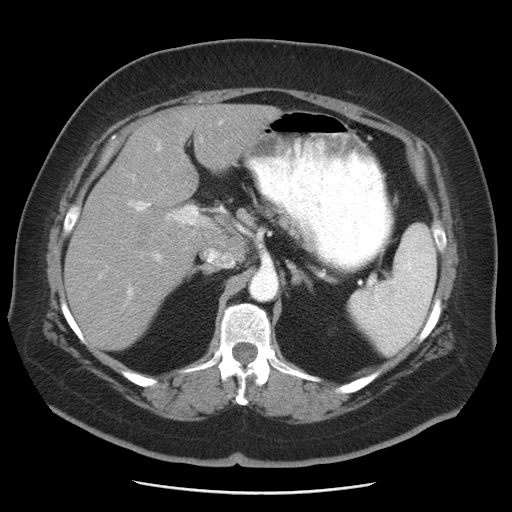
Contrast-enhanced abdominal CT, one axial slice. Slice 30 of 55 in the series (ordered by position). Intravenous contrast given. Soft-tissue window (W 400 / L 40 HU). 5 mm slice thickness. 512 × 512 image matrix. Female patient, age 52 years. From the clinical record (not read from this slice): diagnosis: colorectal cancer liver metastases, imaged before liver resection; multiple liver metastases: yes; largest metastasis: 2.5 cm; disease in both lobes: yes.
Annotated regions visible in this slice (manually delineated by an expert):
- liver: box from (x=65, y=105) to (x=280, y=351) px
- planned liver remnant (the part of the liver to remain after resection): (x=65, y=190)–(x=208, y=351)
- portal vein (with intrahepatic branches): (x=105, y=138)–(x=206, y=296)